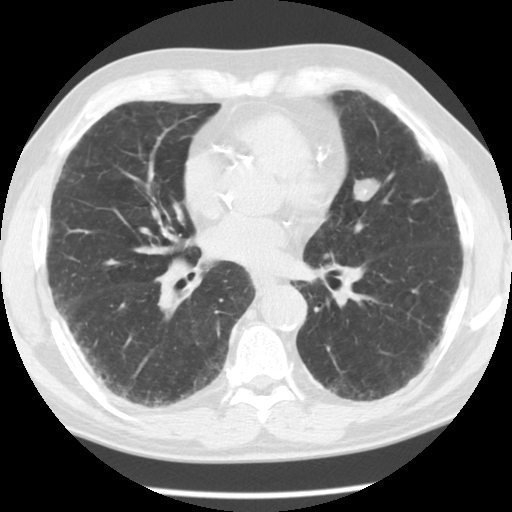
Low-dose screening chest CT, one axial slice; position 53 of 113 along the scan axis; reconstruction kernel STANDARD; lung window (W 1500 / L -600 HU); 512 × 512 image matrix.
Annotated regions visible in this slice (expert manual segmentation):
- lesion 1 (nodule, upper lobe of left lung): bounding box [x1, y1, x2, y2] px = [353, 178, 380, 202]